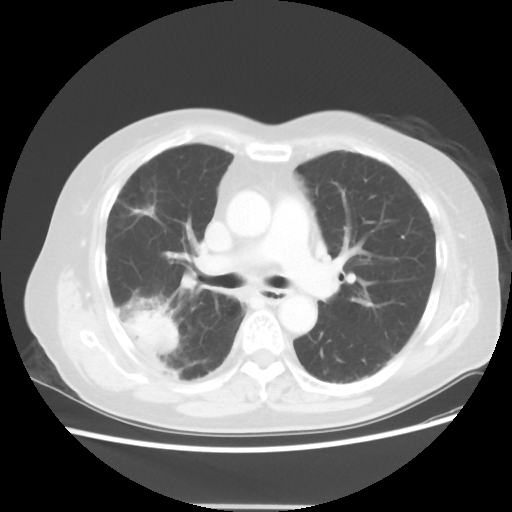
Chest CT, one axial slice; position 29 of 50 along the scan axis; lung window (W 1500 / L -600 HU); 5 mm slice thickness; 512 × 512 image matrix, field of view 360 × 360 mm. Patient: female, 72 years. From the clinical record (not read from this slice): clinical TNM (as recorded): T2 N1 M0.
Outlined on this slice (rectangle marked by the reading radiologist):
- lung tumour (recorded histology: adenocarcinoma): bounding box (x1, y1, x2, y2) in pixels: (124, 308, 179, 353)